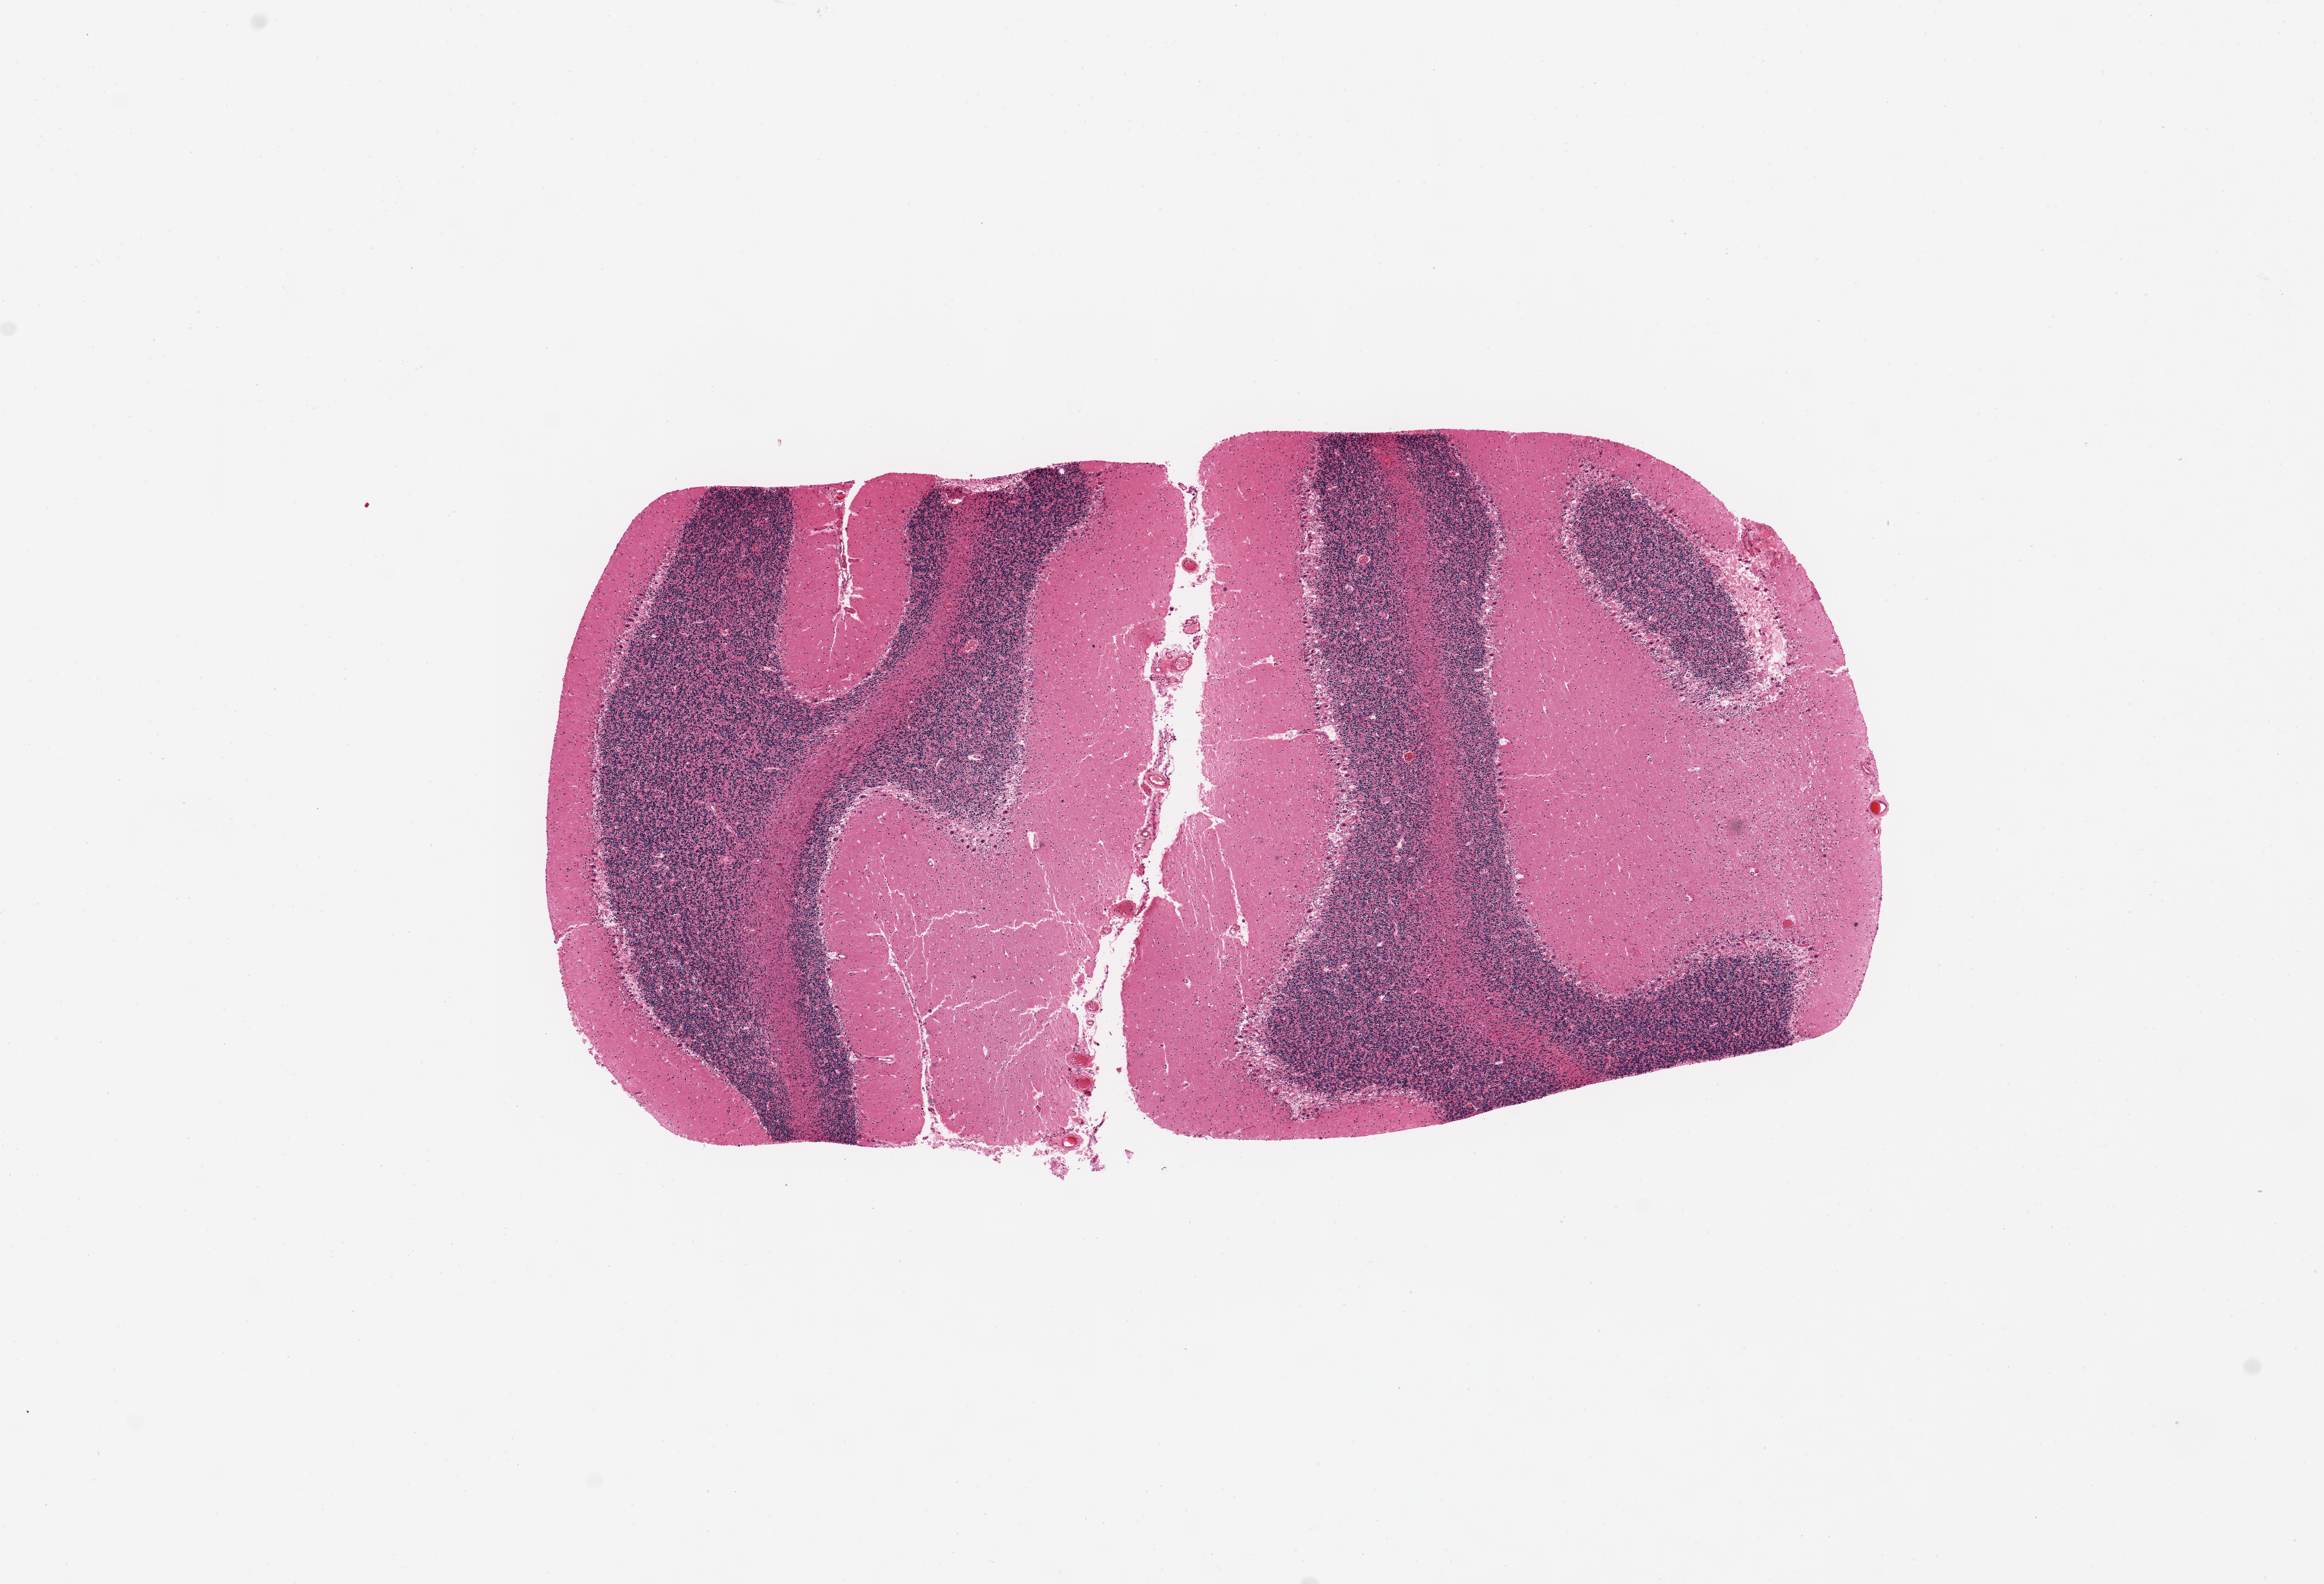
Whole-slide image, H&E stain — shown as a low-resolution overview of the whole scanned area (about 13.8 x 9.4 mm, slide scanned at 20x); PAXgene-fixed, paraffin-embedded tissue; target tissue: cerebellum; tissue donor sample.
Review note (as recorded): 1 piece 7.8x4 mm.